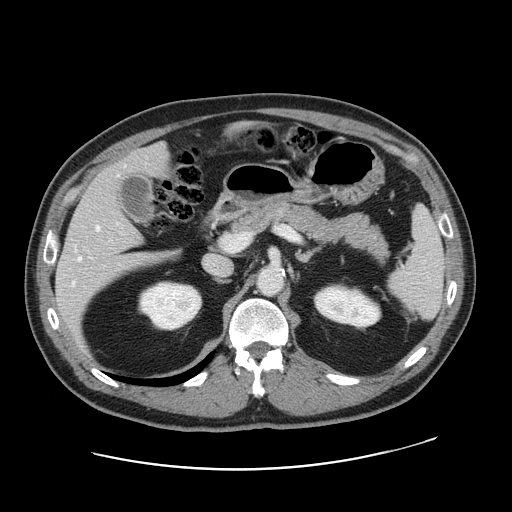
Contrast-enhanced abdominal CT, one axial slice. Slice 92 of 178 in the series (ordered by position). 120 kVp. Intravenous contrast given. Soft-tissue window (W 400 / L 40 HU). 2.5 mm slice thickness. 512 × 512 image matrix. Male patient, age 63 years. Case-level facts recorded for this patient, not image findings: diagnosis: colorectal cancer liver metastases, imaged before liver resection; multiple liver metastases: yes; largest metastasis: 8 cm; chemotherapy before resection: no.
Annotated regions visible in this slice (manually delineated by an expert):
- hepatic veins: bounding box [x1, y1, x2, y2] px = [73, 226, 100, 284]
- liver: [57, 144, 169, 334]
- planned liver remnant (the part of the liver to remain after resection): [117, 144, 169, 178]
- portal vein (with intrahepatic branches): [222, 232, 252, 252]